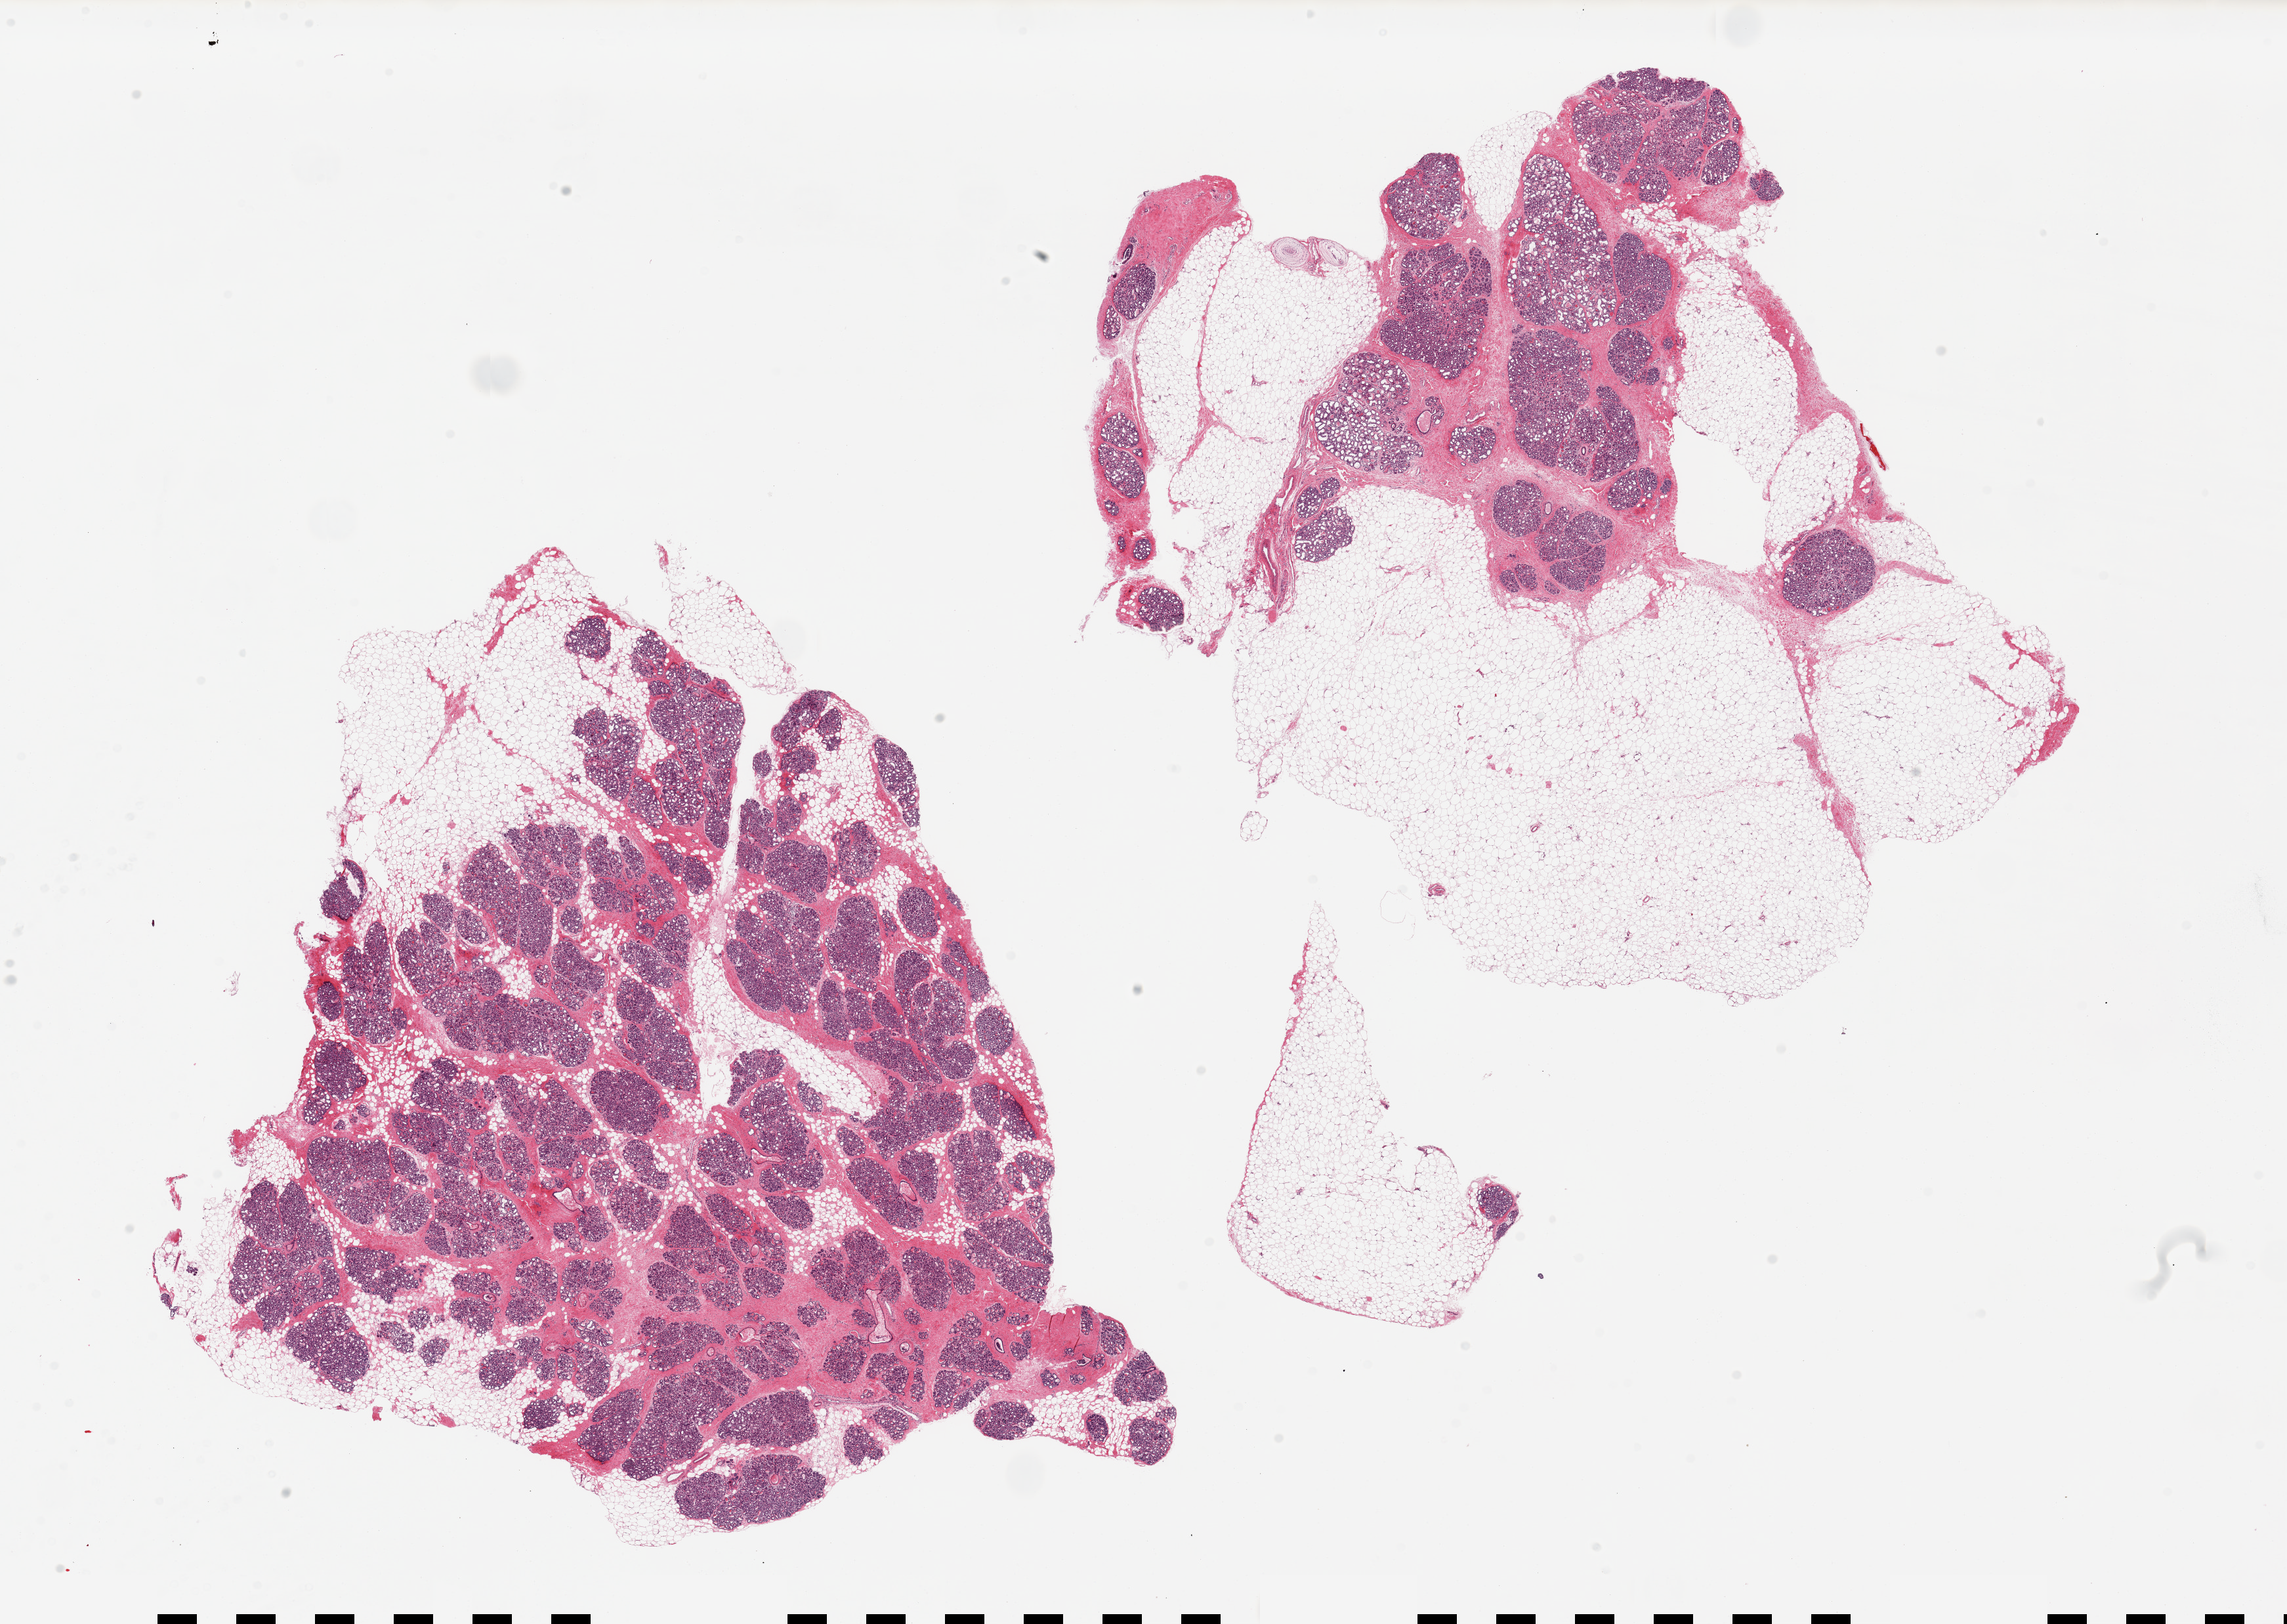
Whole-slide image, hematoxylin and eosin (H&E) stain, shown as a low-resolution overview of the whole scanned area (about 27.6 x 19.6 mm, acquisition: 20x scan), PAXgene-fixed paraffin-embedded (PFPE) section, sampled site (target tissue): breast, tissue donor sample. Female donor.
- reviewer comment on this tissue sample: 2 pieces, 14x11 & 14x12mm; extensive microglandular adenosis, well- preserved